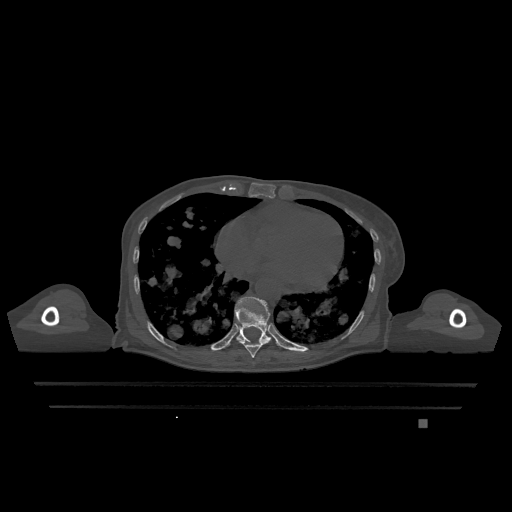
CT including the spine, one axial slice. Slice 669 of 1317 in the series (ordered by position). Bone window (W 1800 / L 400 HU). 512 × 512 image matrix, field of view 500 × 500 mm. Patient: female, 74 years. From the clinical record (not read from this slice): primary cancer: lung; vertebrae with lytic lesions (as recorded): T1, T4, T5, T6, L4, L5.
Annotated regions visible in this slice (semi-automatically segmented with operator editing):
- T10 vertebra: bounding box [x1, y1, x2, y2] px = [235, 296, 271, 342]
- T9 vertebra: [236, 338, 271, 358]